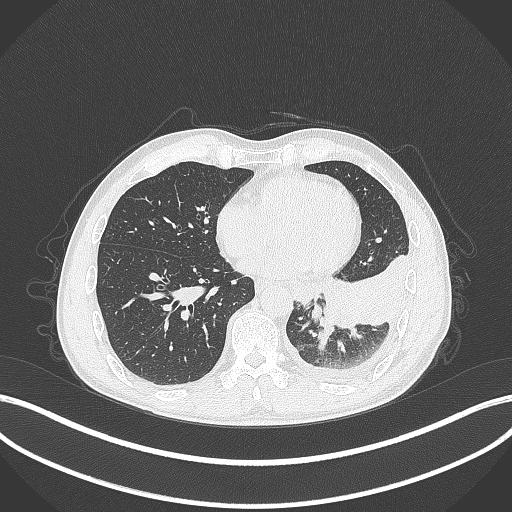
Chest CT, one axial slice. Position 103 of 295 along the scan axis. 120 kVp. Lung window (W 1500 / L -600 HU). 512 × 512 image matrix. Male patient, age 47 years. From the clinical record (not read from this slice): clinical TNM (as recorded): T3 N1 M1c; histopathological grade: G3.
Annotated regions visible in this slice (rectangle marked by the reading radiologist):
- lung tumour (recorded histology: small cell carcinoma): bounding box (x1, y1, x2, y2) in pixels: (318, 311, 332, 333)